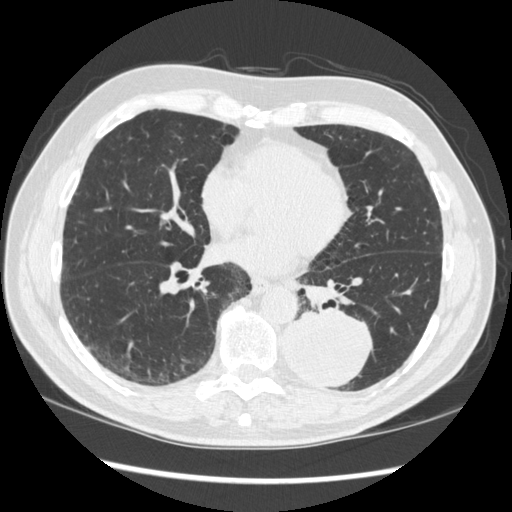
Chest CT (low-dose screening protocol), one axial image; baseline annual screen; lung window (W 1500 / L -600 HU); 1.25 mm slice thickness; standard (soft-tissue) reconstruction kernel (STANDARD); slice 138 of 348 in the series; 512 × 512 image matrix, field of view 360 × 360 mm. Male, age 72 years at enrolment. Current smoker at enrolment.
- Expert-annotated lung lesion, bounding box [x1, y1, x2, y2] px = [270, 300, 374, 390].
- The screening reader recorded 2 non-calcified nodules or masses ≥4 mm on this exam; which of them this box marks is not recorded.
- Participant outcome: lung cancer diagnosed 37 days after this screen — squamous cell carcinoma, NOS, left lower lobe, stage IIIA (AJCC 6th edition), 60 mm at pathology.